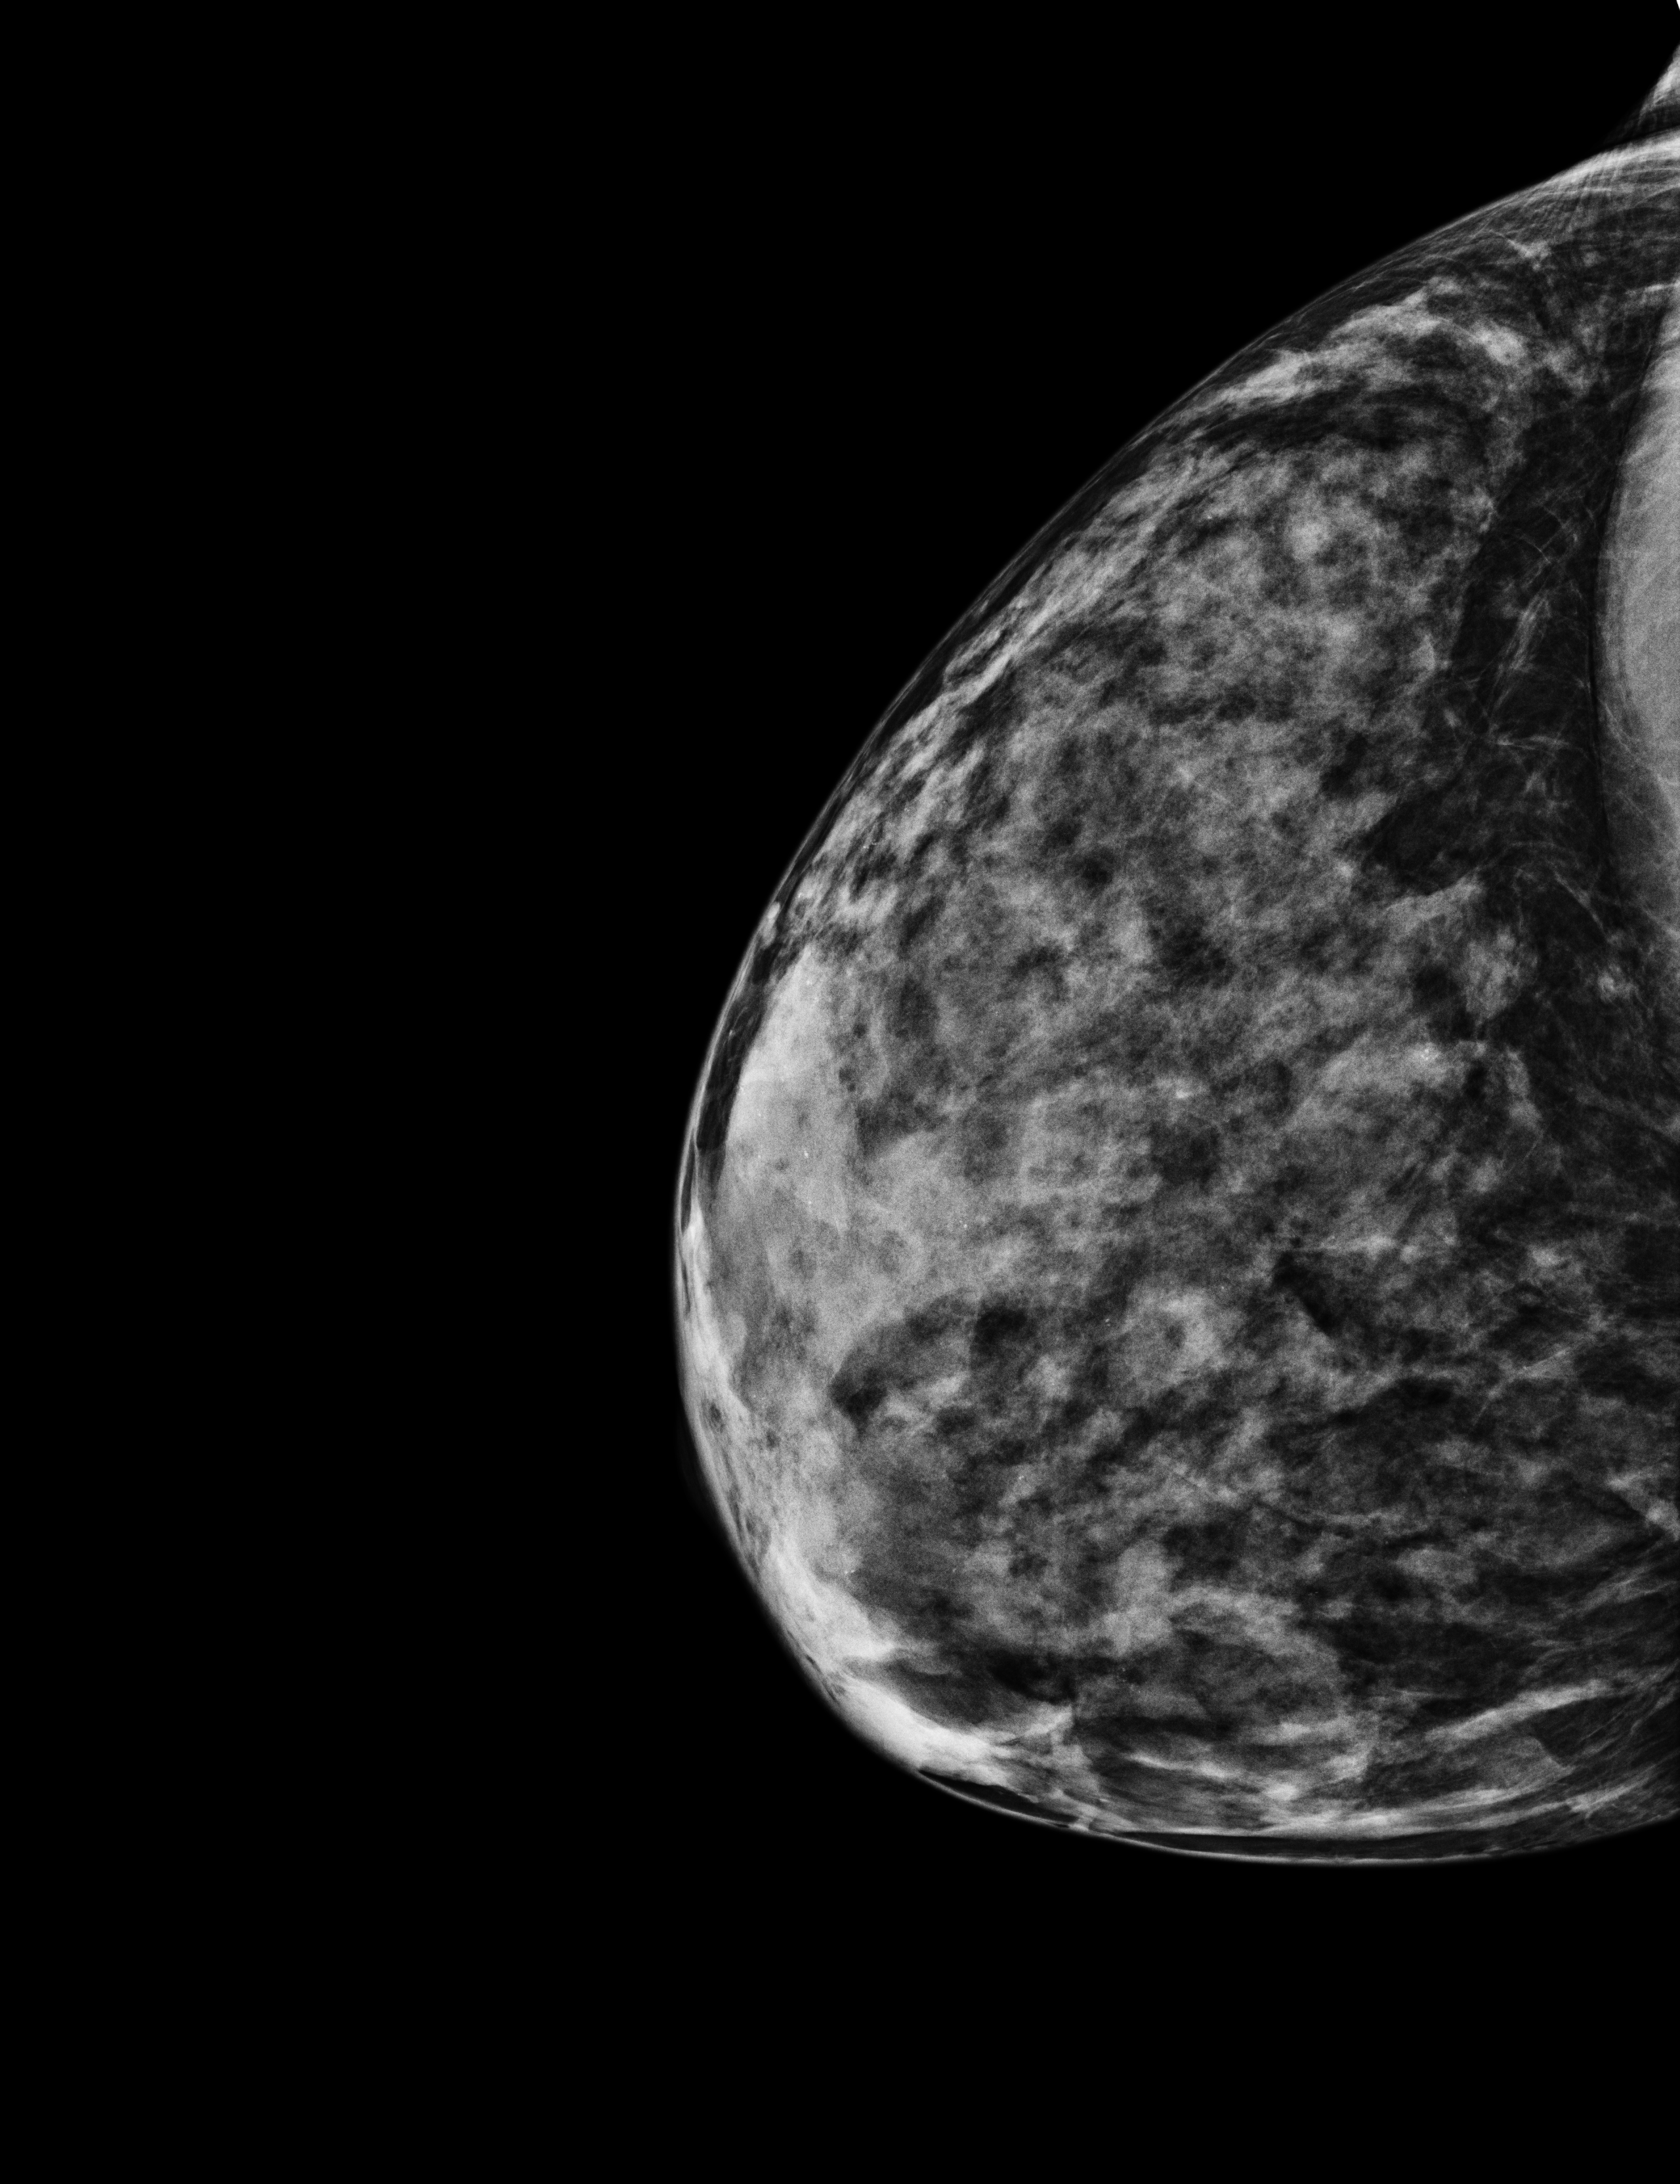
Digital mammogram (FFDM), right breast, laterally exaggerated craniocaudal (XCCL) view, screening examination, compressed breast thickness 34 mm. Female patient, age 43 years.
Breast density at the screening exam (both breasts): extremely dense (BI-RADS density category d). Final BI-RADS assessment for this screening round (tomosynthesis exam, both breasts): category 2. Recall: no recall after this screen.